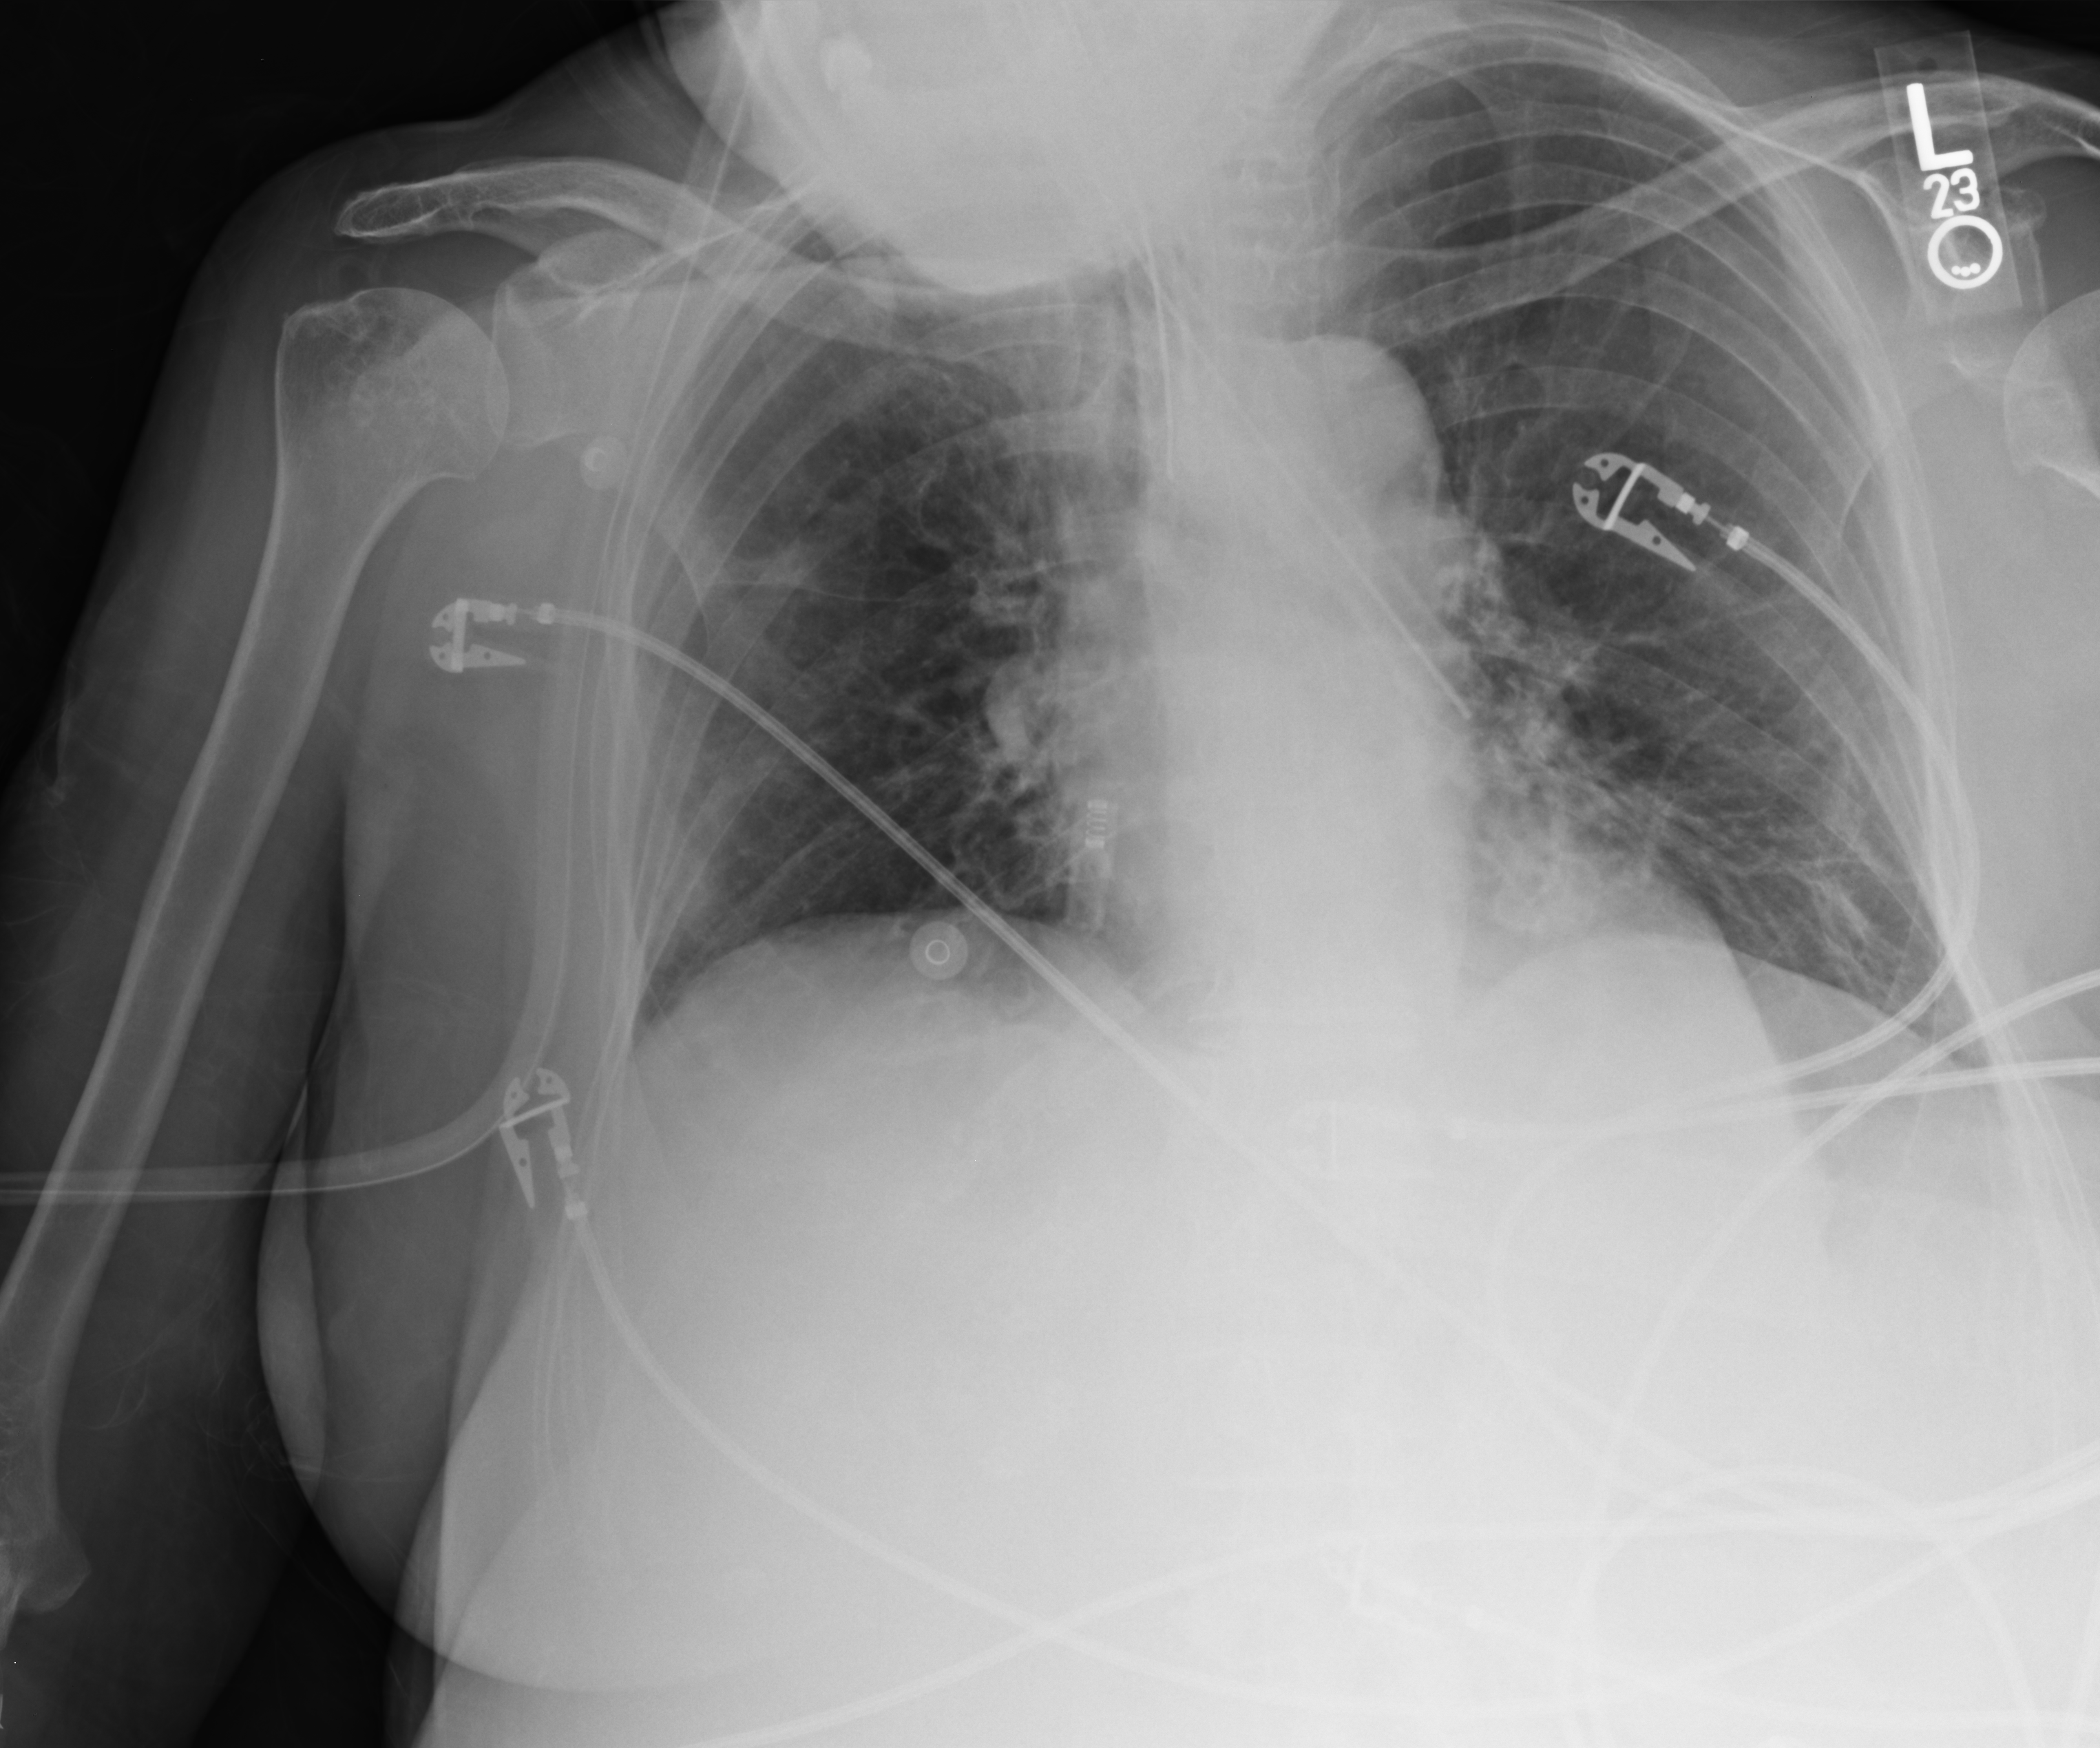
Bedside chest radiograph (computed radiography); anteroposterior (AP) projection. Patient hospitalised with COVID-19; female, aged 75–90 years.
Admission-level facts for this patient (not findings on this image; timing relative to this image not recorded):
- chronic kidney disease (admission record): yes